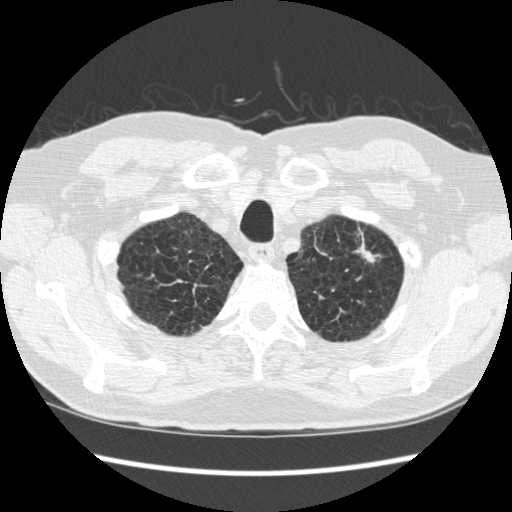
Axial slice from a low-dose chest CT screening exam, second annual screen, lung window (W 1500 / L -600 HU), standard (soft-tissue) reconstruction kernel (STANDARD), 120 kVp, slice 38 of 295 in the series, 512 × 512 image matrix. Male participant, aged 70 years at enrolment. Former smoker at enrolment.
• Expert-annotated lung lesion, bounding box (x1, y1, x2, y2) in pixels: (327, 227, 389, 295).
• The screening reader recorded 5 non-calcified nodules or masses ≥4 mm on this exam (right lower lobe, right lower lobe, right lower lobe, left upper lobe, left lower lobe); which of them this box marks is not recorded.
• Official screen result: positive, change unspecified: nodule(s) >= 4 mm or enlarging nodule(s), mass(es), or other non-specific abnormalities suspicious for lung cancer.
• Lung cancer was diagnosed 479 days after this screen (after the third annual screen): squamous cell carcinoma, NOS, left upper lobe, moderately differentiated (G2), stage IA (AJCC 6th edition), 18 mm at pathology.